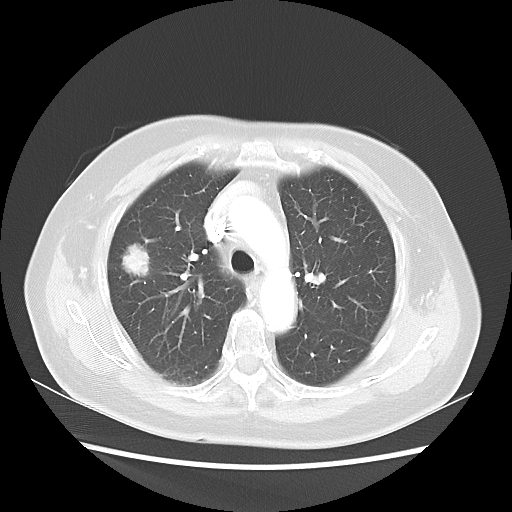
Chest CT, one axial slice; position 33 of 48 along the scan axis; lung window (W 1500 / L -600 HU); 512 × 512 image matrix. Female patient, age 75 years. From the clinical record (not read from this slice): clinical TNM (as recorded): T1c N0 M0.
Annotated regions visible in this slice (rectangle marked by the reading radiologist):
- lung tumour (recorded histology: adenocarcinoma): bounding box (x1, y1, x2, y2) in pixels: (116, 236, 156, 283)